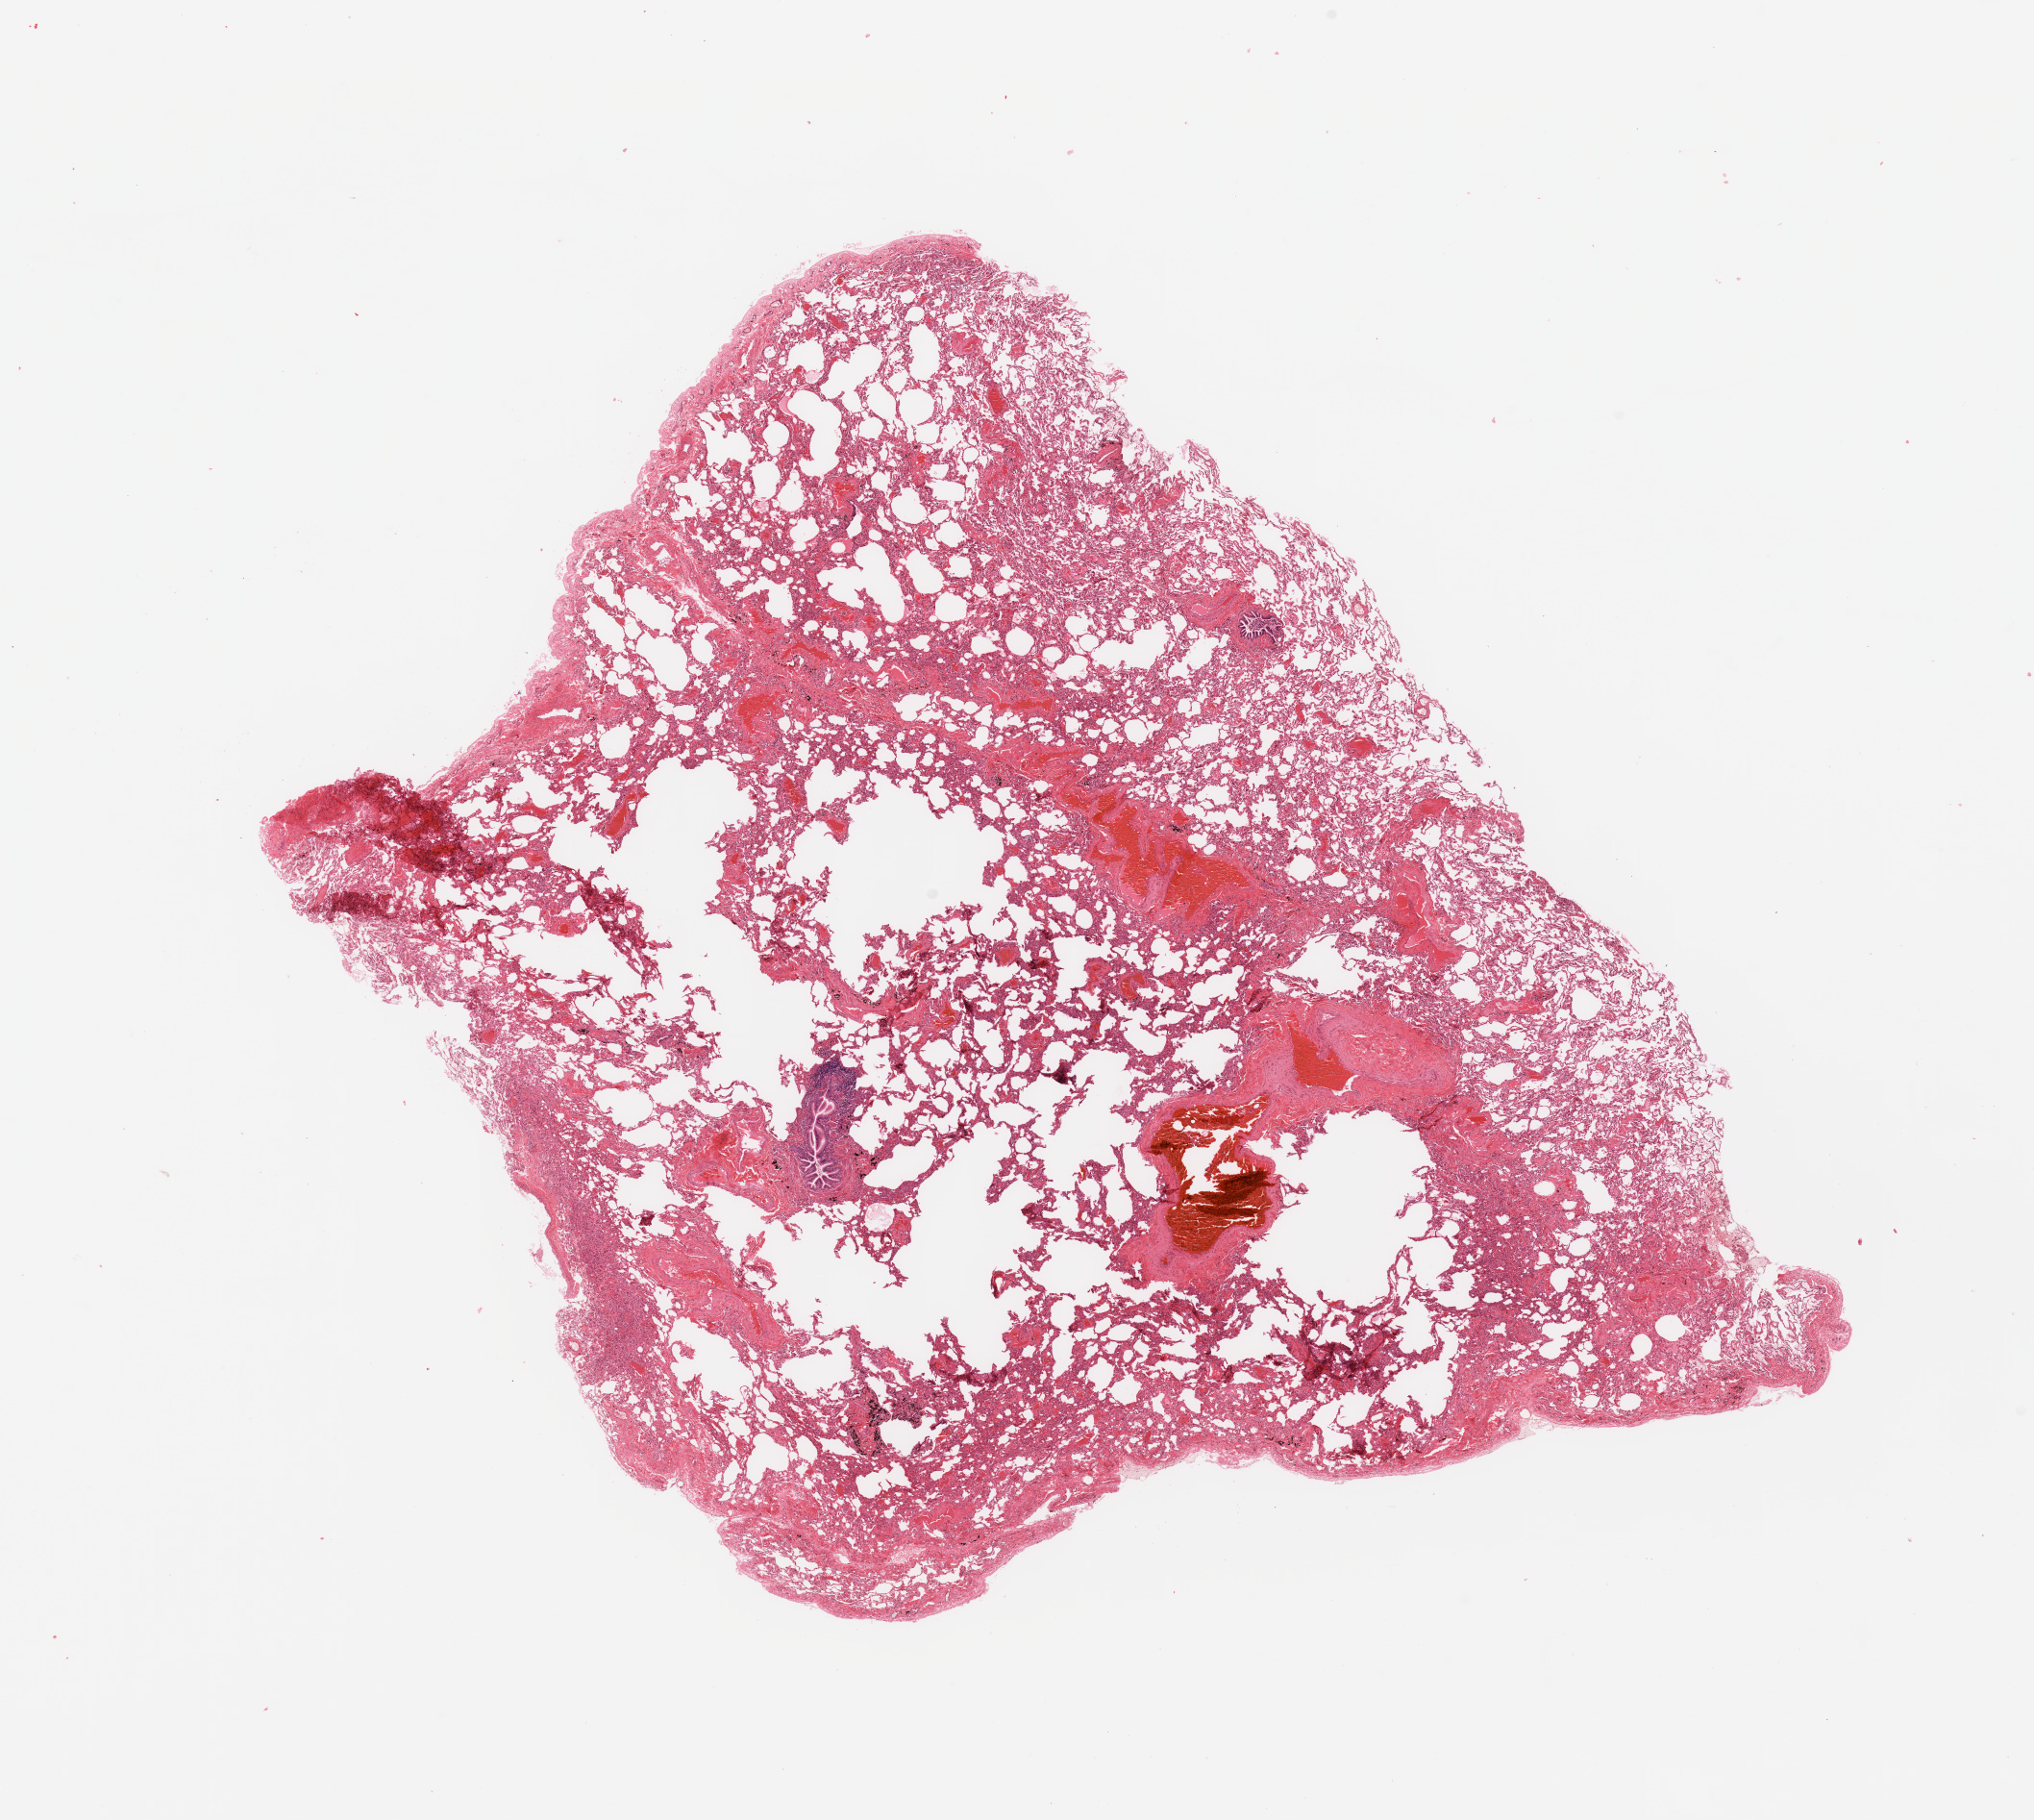
H&E whole-slide image, whole scanned area (about 16.7 x 15.0 mm, slide scanned at 20x) shown as a low-resolution overview; normal (non-tumour) tissue sample, lung. Patient: female, age 52 years.
This section: normal (non-tumour) tissue from the same patient. Patient diagnosis: Adenocarcinoma, NOS.